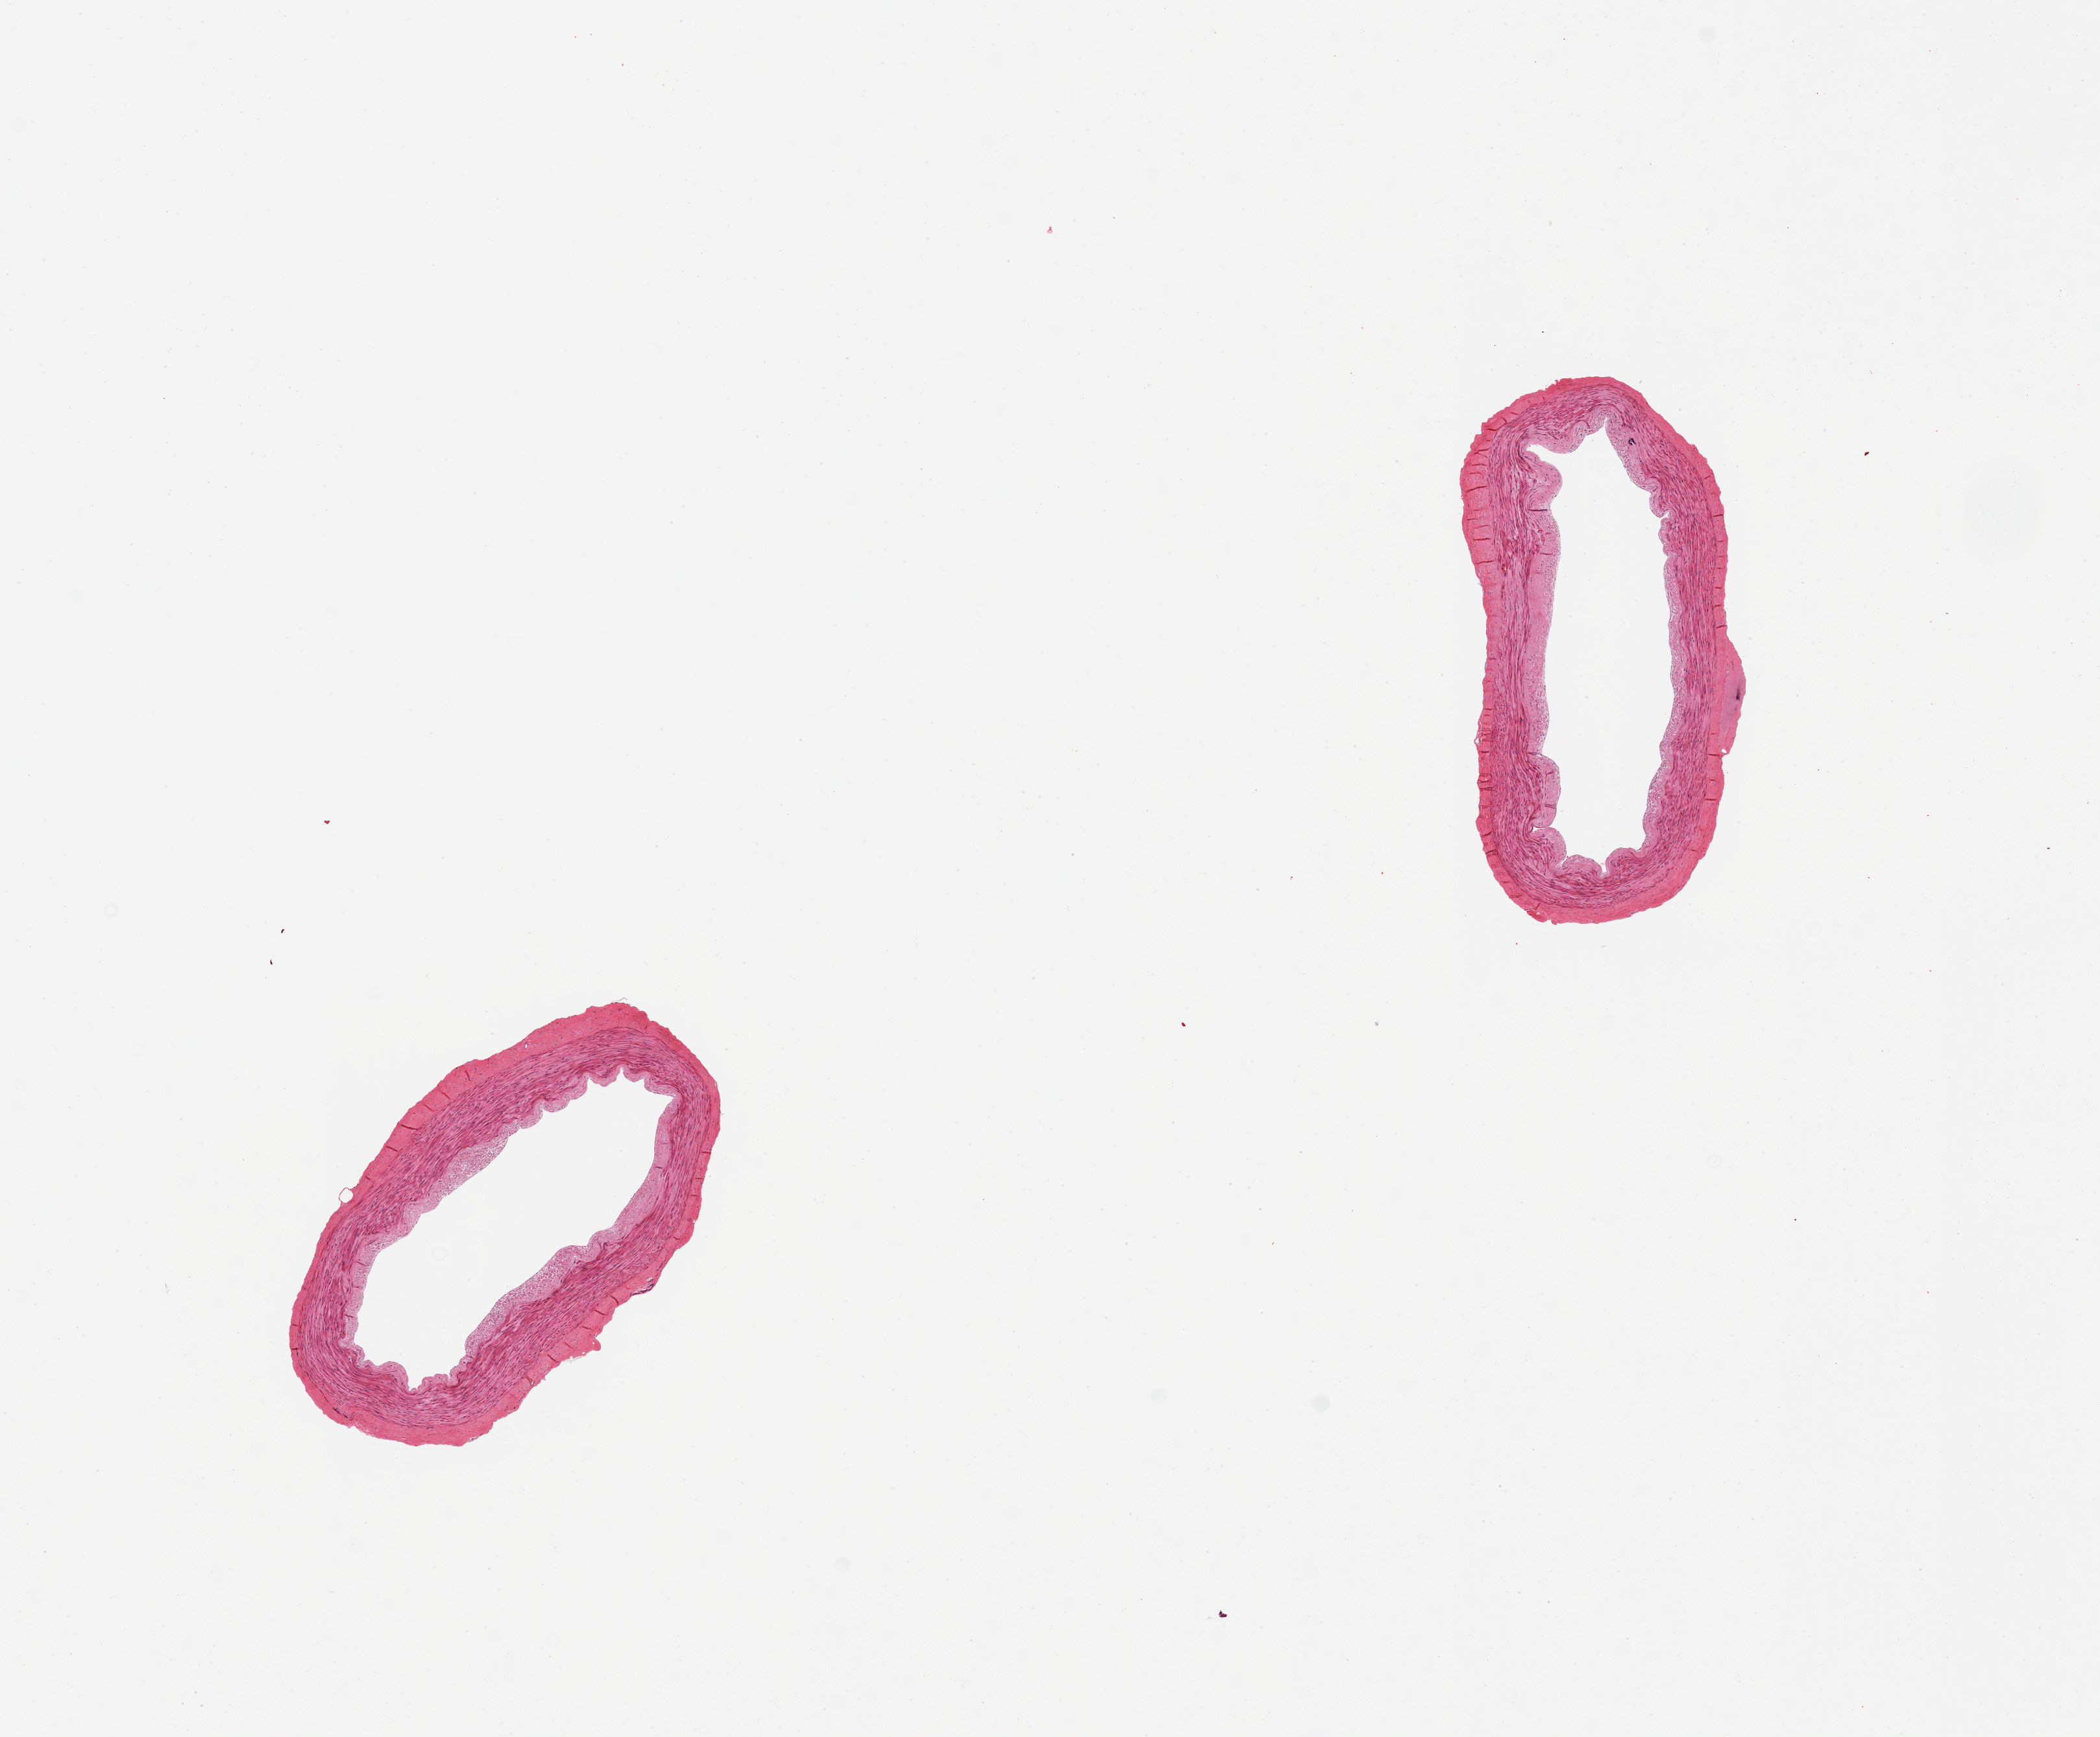
H&E whole-slide image — shown as a low-resolution overview of the whole scanned area (about 12.8 x 10.6 mm), PAXgene-fixed, paraffin-embedded tissue, target tissue: tibial artery, donor tissue sample. Male donor.
- reviewer comment on this tissue sample: 2 pieces, excellent specimen, some intimal thickening and small focus of medial calcification